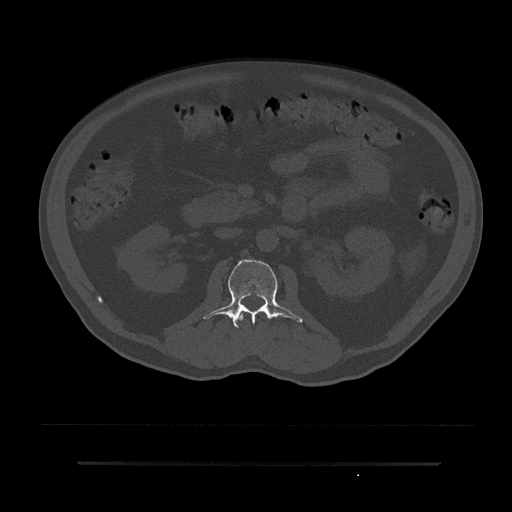
CT including the spine, one axial slice. Position 83 of 797 along the scan axis. Bone window (W 1800 / L 400 HU). 0.5 mm slice thickness. 512 × 512 image matrix, field of view 464 × 464 mm. Male patient, age 59 years. From the clinical record (not read from this slice): primary cancer: bile ducts; vertebrae with lytic lesions (as recorded): T10.
Structures marked on this image (semi-automatic segmentation, software-assisted and operator-edited):
- L1 vertebra: bounding box (x1, y1, x2, y2) in pixels: (236, 311, 245, 326)
- L2 vertebra: (203, 259, 303, 328)